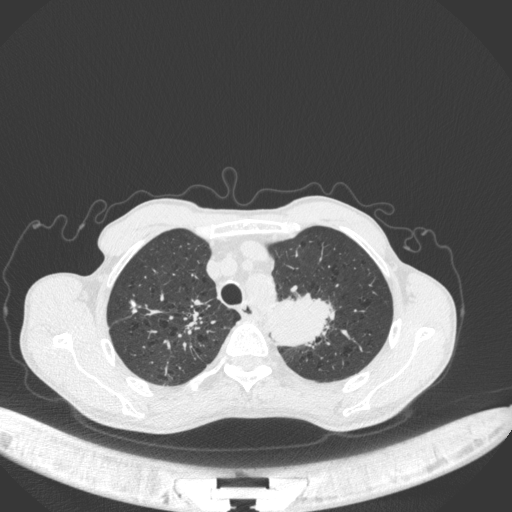
Chest CT, one axial slice. Slice 343 of 394 in the series (ordered by position). 120 kVp. Lung window (W 1500 / L -600 HU). 1 mm slice thickness. 512 × 512 image matrix, field of view 400 × 400 mm. Male patient, age 65 years. From the clinical record (not read from this slice): clinical TNM (as recorded): T2b N0 M0.
Annotated regions visible in this slice (bounding box drawn by a radiologist):
- lung tumour (recorded histology: adenocarcinoma): bounding box <269,289,336,347> (left, top, right, bottom; pixels)